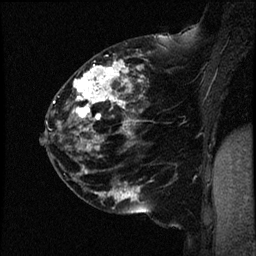
Breast MRI (dynamic contrast-enhanced), one sagittal slice. Dynamic contrast-enhanced study with each time point stored as its own series, time point 2 of 4 at this slice position (early post-contrast, ordered by acquisition time). 1.5 T. TE 4.2 ms, TR 17.7 ms. 2 mm slice thickness. 256 × 256 image matrix, field of view 200 × 200 mm. Female patient, age 52 years. From the clinical record (not read from this slice): setting: breast cancer imaged before/during neoadjuvant chemotherapy; receptor status: HR-positive, HER2-negative.
Outlined on this slice (semi-automatic segmentation, software-assisted and operator-edited):
- analysis volume of interest (the breast-tissue region the enhancement analysis was run in; not a lesion): box from (x=47, y=48) to (x=163, y=147) px
- tumour enhancement mask (voxels above the 100 % enhancement threshold inside the analysis volume of interest): (x=72, y=62)–(x=144, y=147)